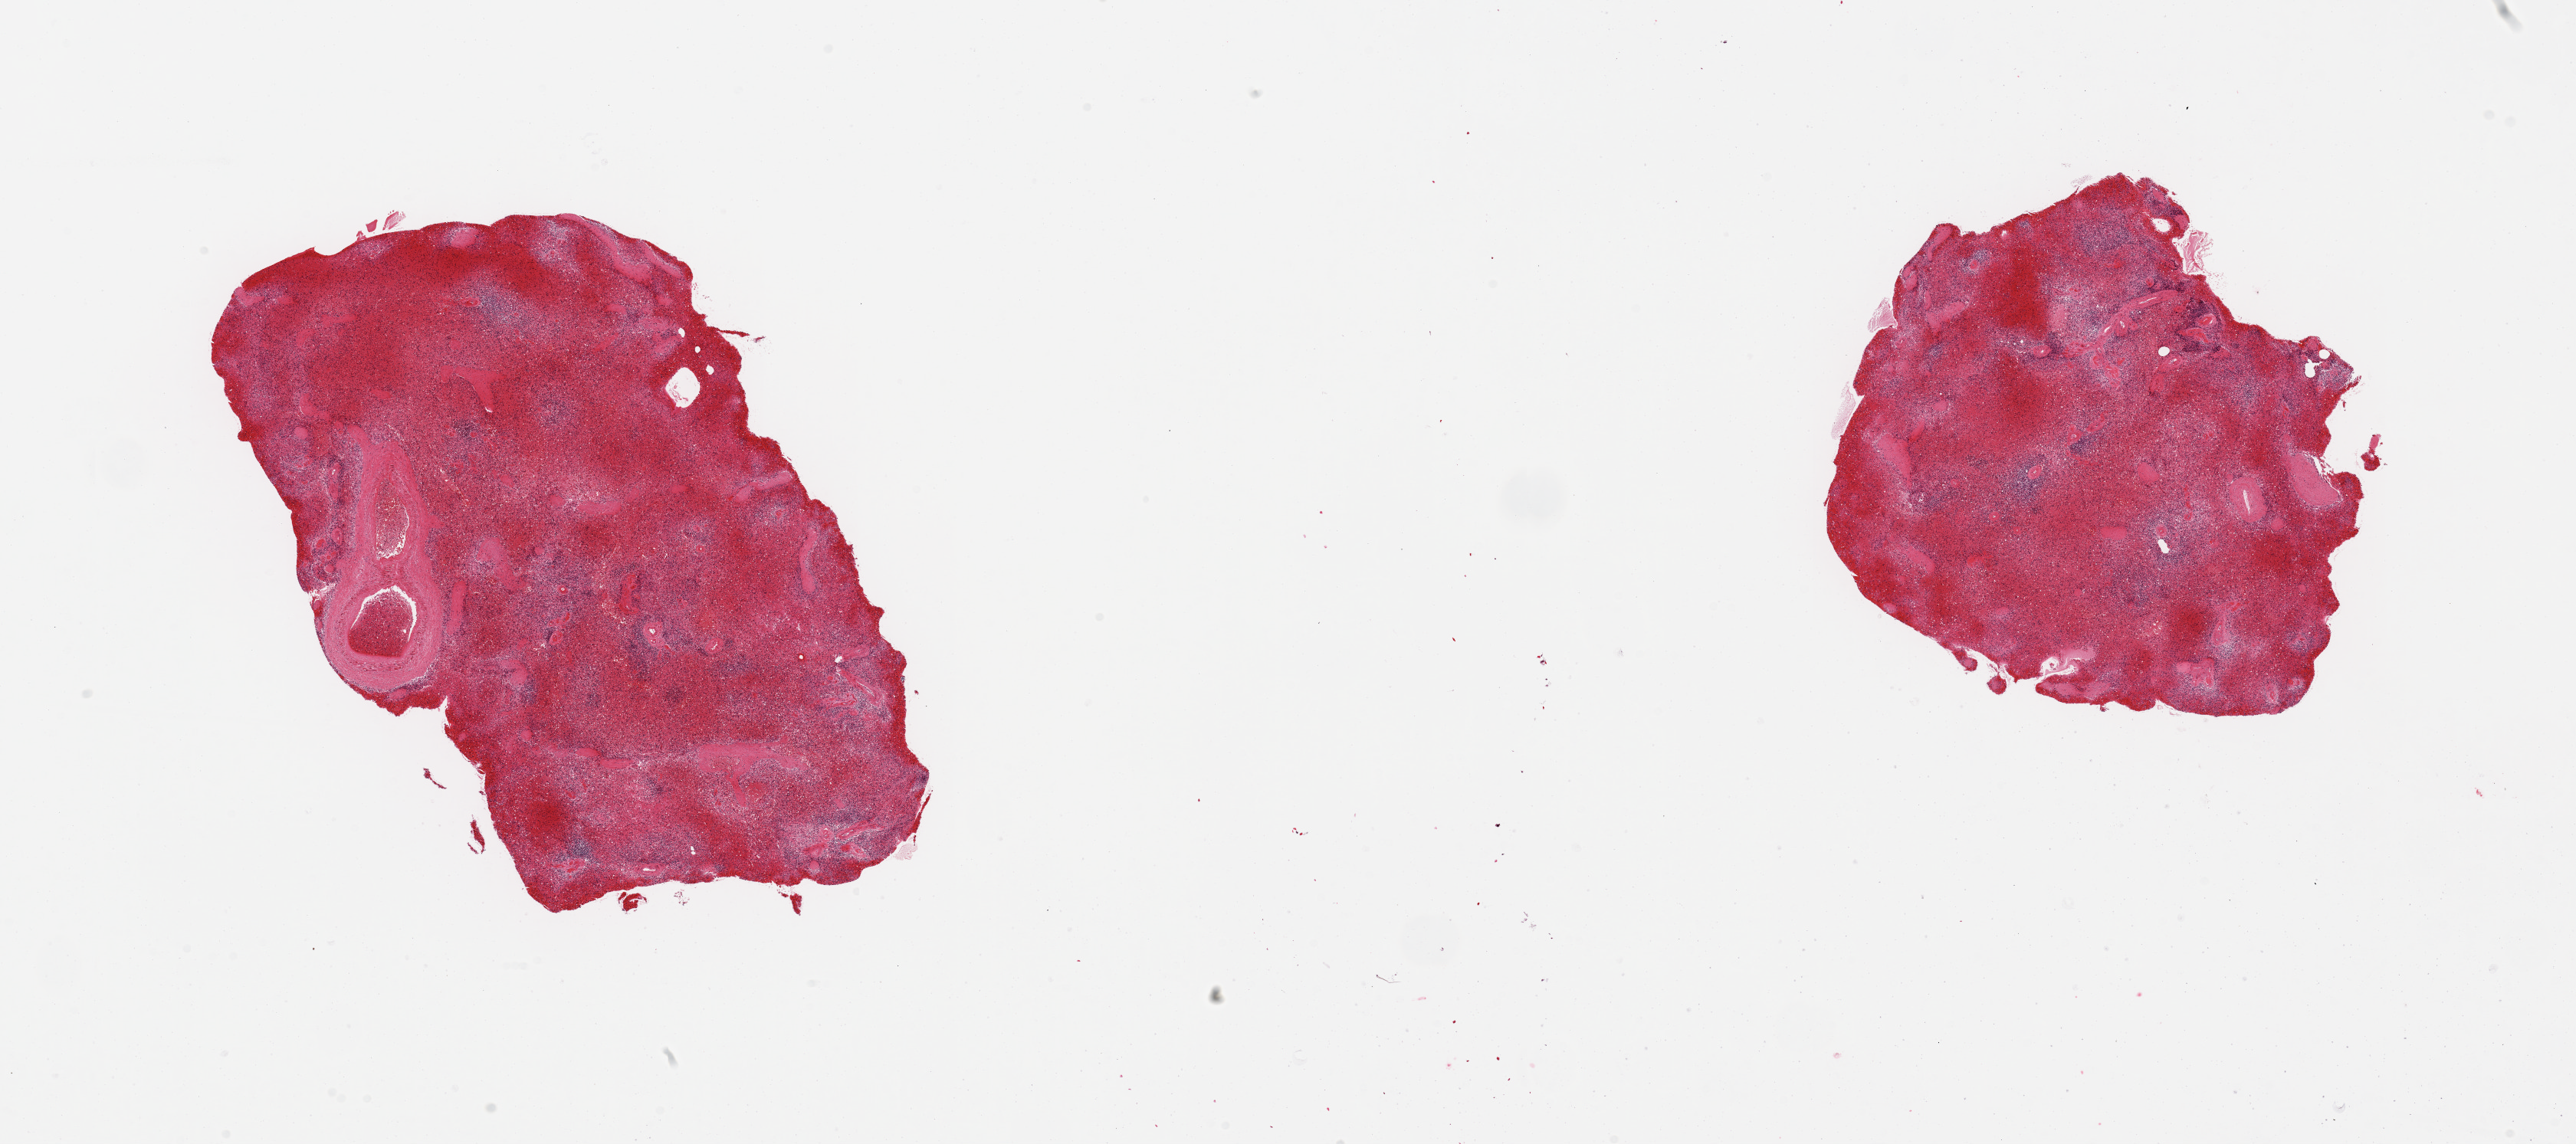
Digitized hematoxylin and eosin (H&E)-stained section — whole scanned area (about 26.6 x 11.8 mm) shown as a low-resolution overview. PAXgene-fixed, paraffin-embedded tissue. Target tissue: spleen. Donor tissue sample. Donor: male.
Pathologist's review note for this sample: 2 pieces, moderate-marked congestion.